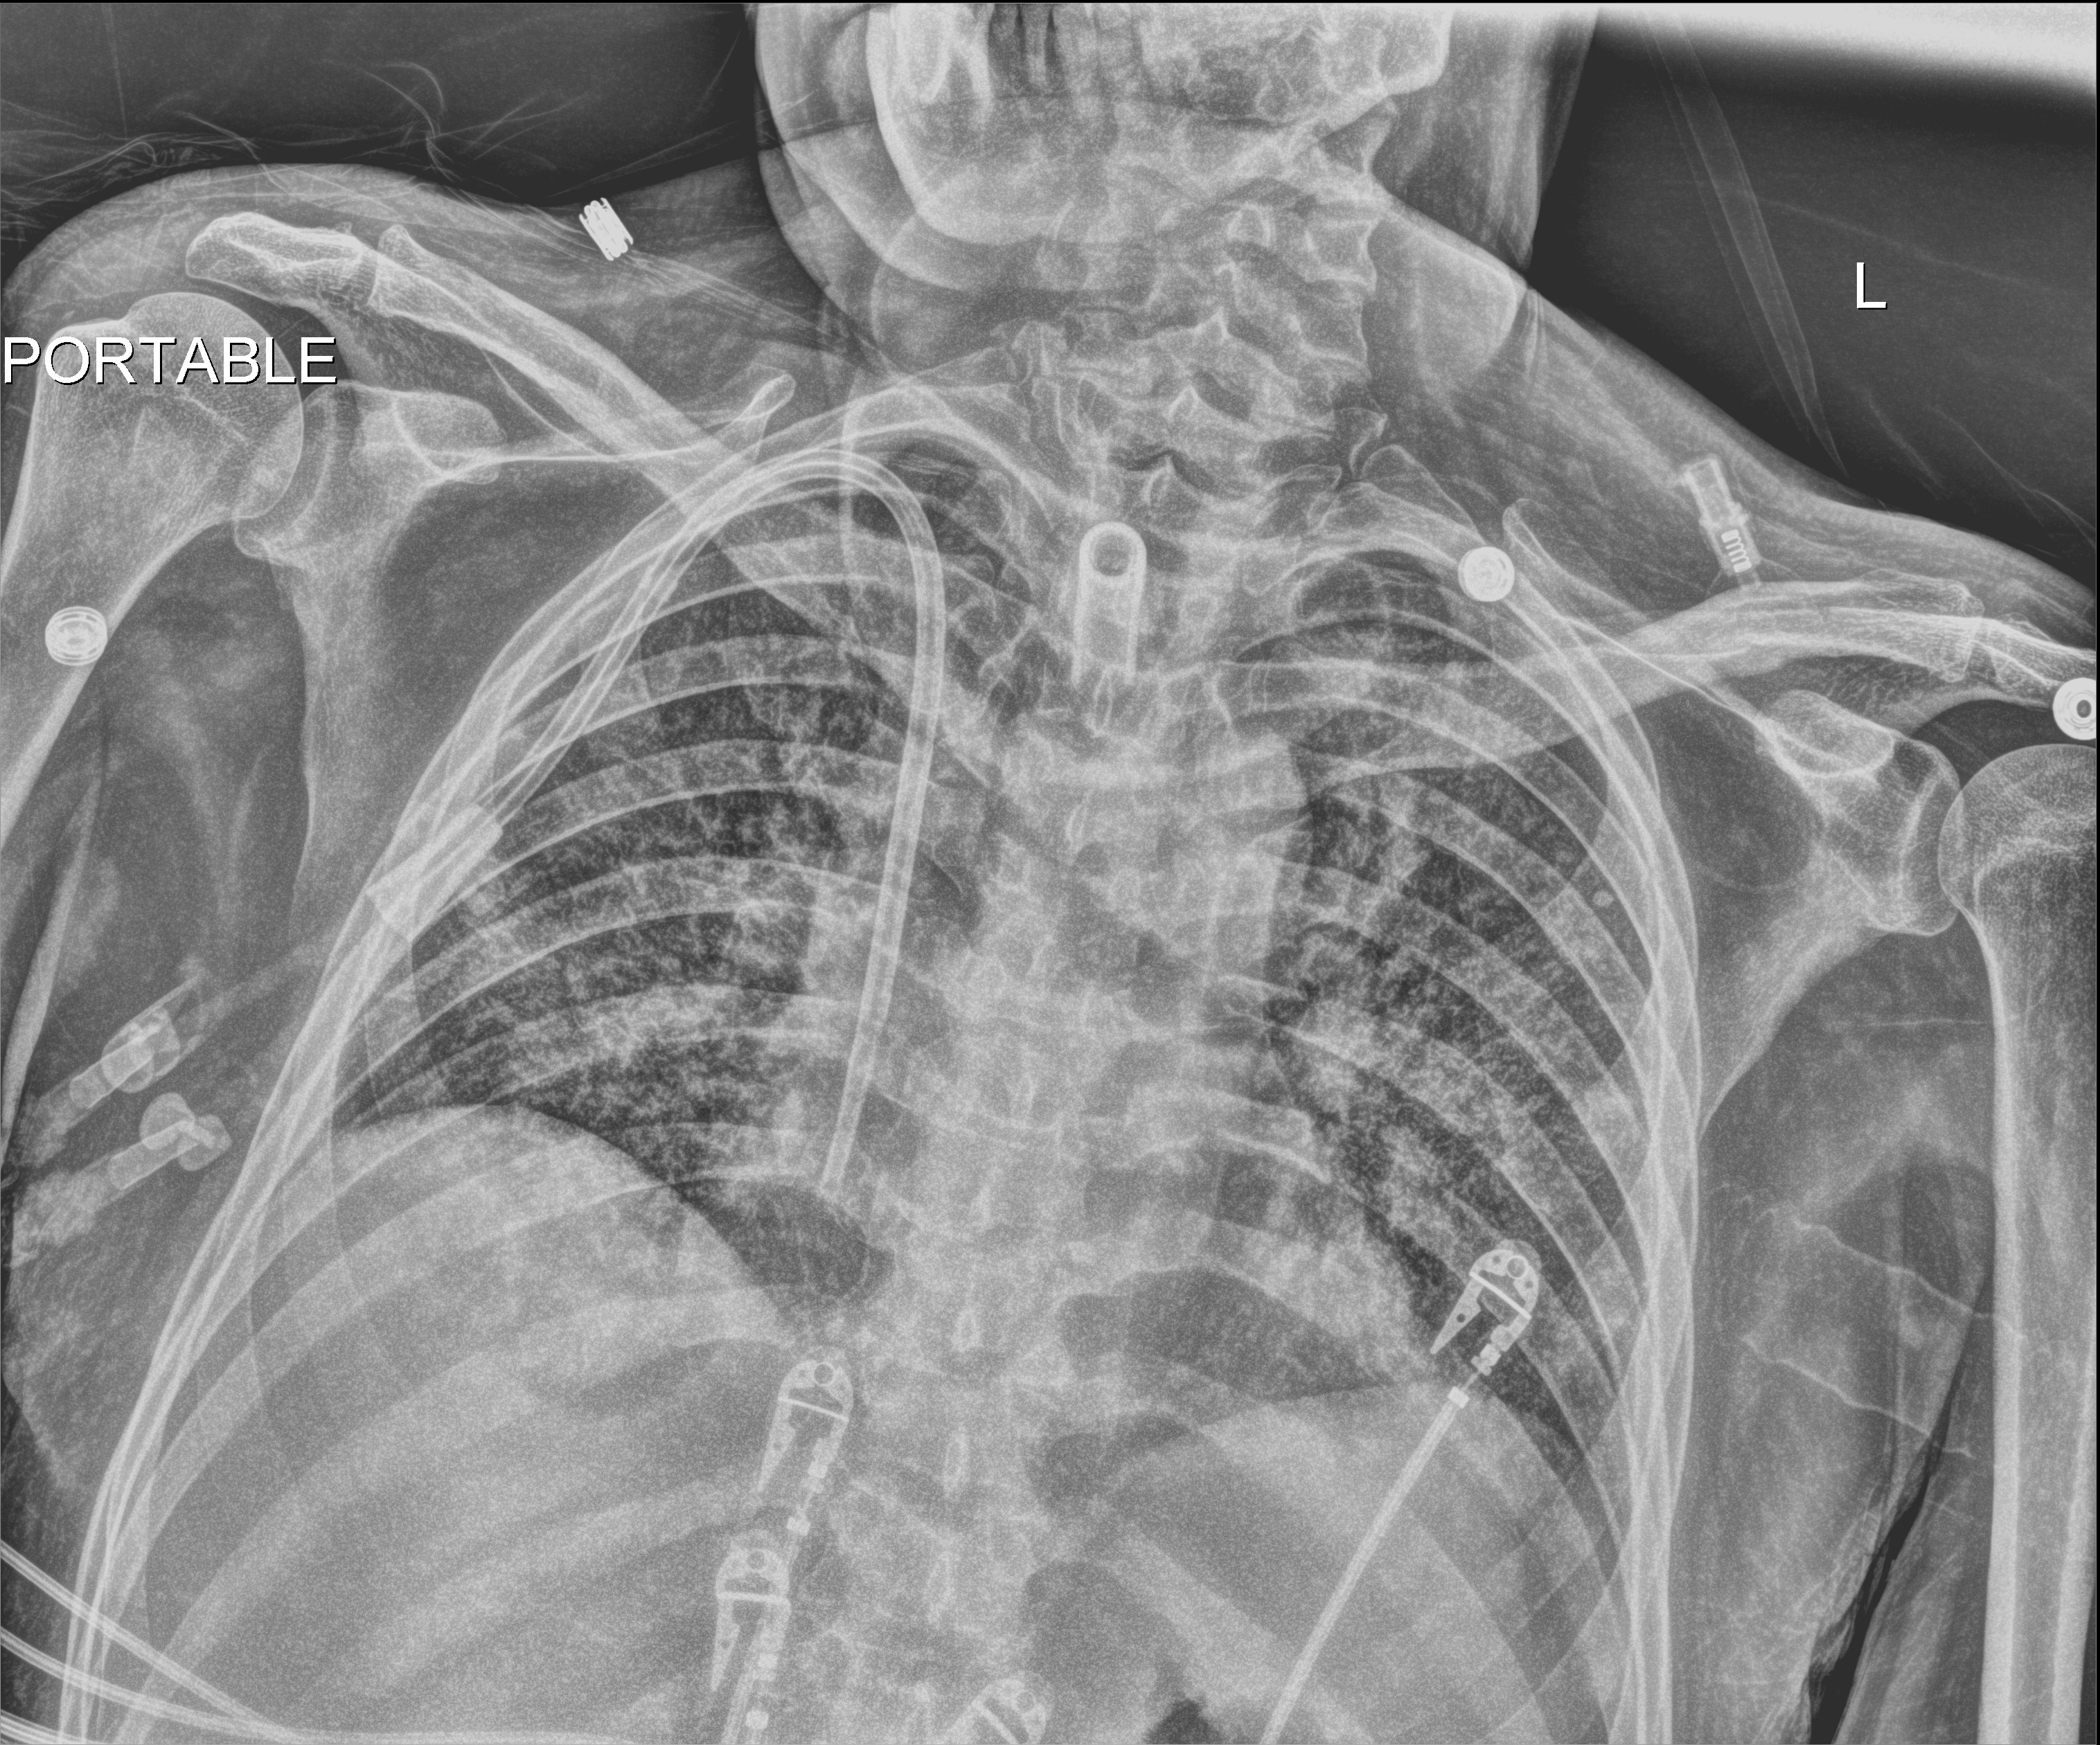
Chest X-ray (portable); anteroposterior (AP) projection. Patient hospitalised with COVID-19; male, aged 18–59 years.
Hospital-stay facts (about this admission, not read from this image; timing relative to this image not recorded):
- mechanically ventilated during this hospital stay: yes
- smoking status (admission record): never
- diabetes (admission record): no